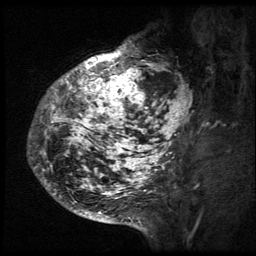
Breast MRI (dynamic contrast-enhanced), one sagittal slice. Slice 17 of 64 in the series (ordered by position). 3 images stored at this slice position (order not interpretable as contrast timing). 1.5 T. TE 4.2 ms, TR 9 ms. 2.5 mm slice thickness. 256 × 256 image matrix. Patient: female, 50 years. Case-level facts recorded for this patient, not image findings: setting: breast cancer imaged before/during neoadjuvant chemotherapy; receptor status: triple-negative.
Outlined on this slice (semi-automatic segmentation, software-assisted and operator-edited):
- analysis volume of interest (the breast-tissue region the enhancement analysis was run in; not a lesion): bounding box <27,39,194,212> (left, top, right, bottom; pixels)
- tumour enhancement mask (voxels above the 140 % enhancement threshold inside the analysis volume of interest): <29,39,194,212>